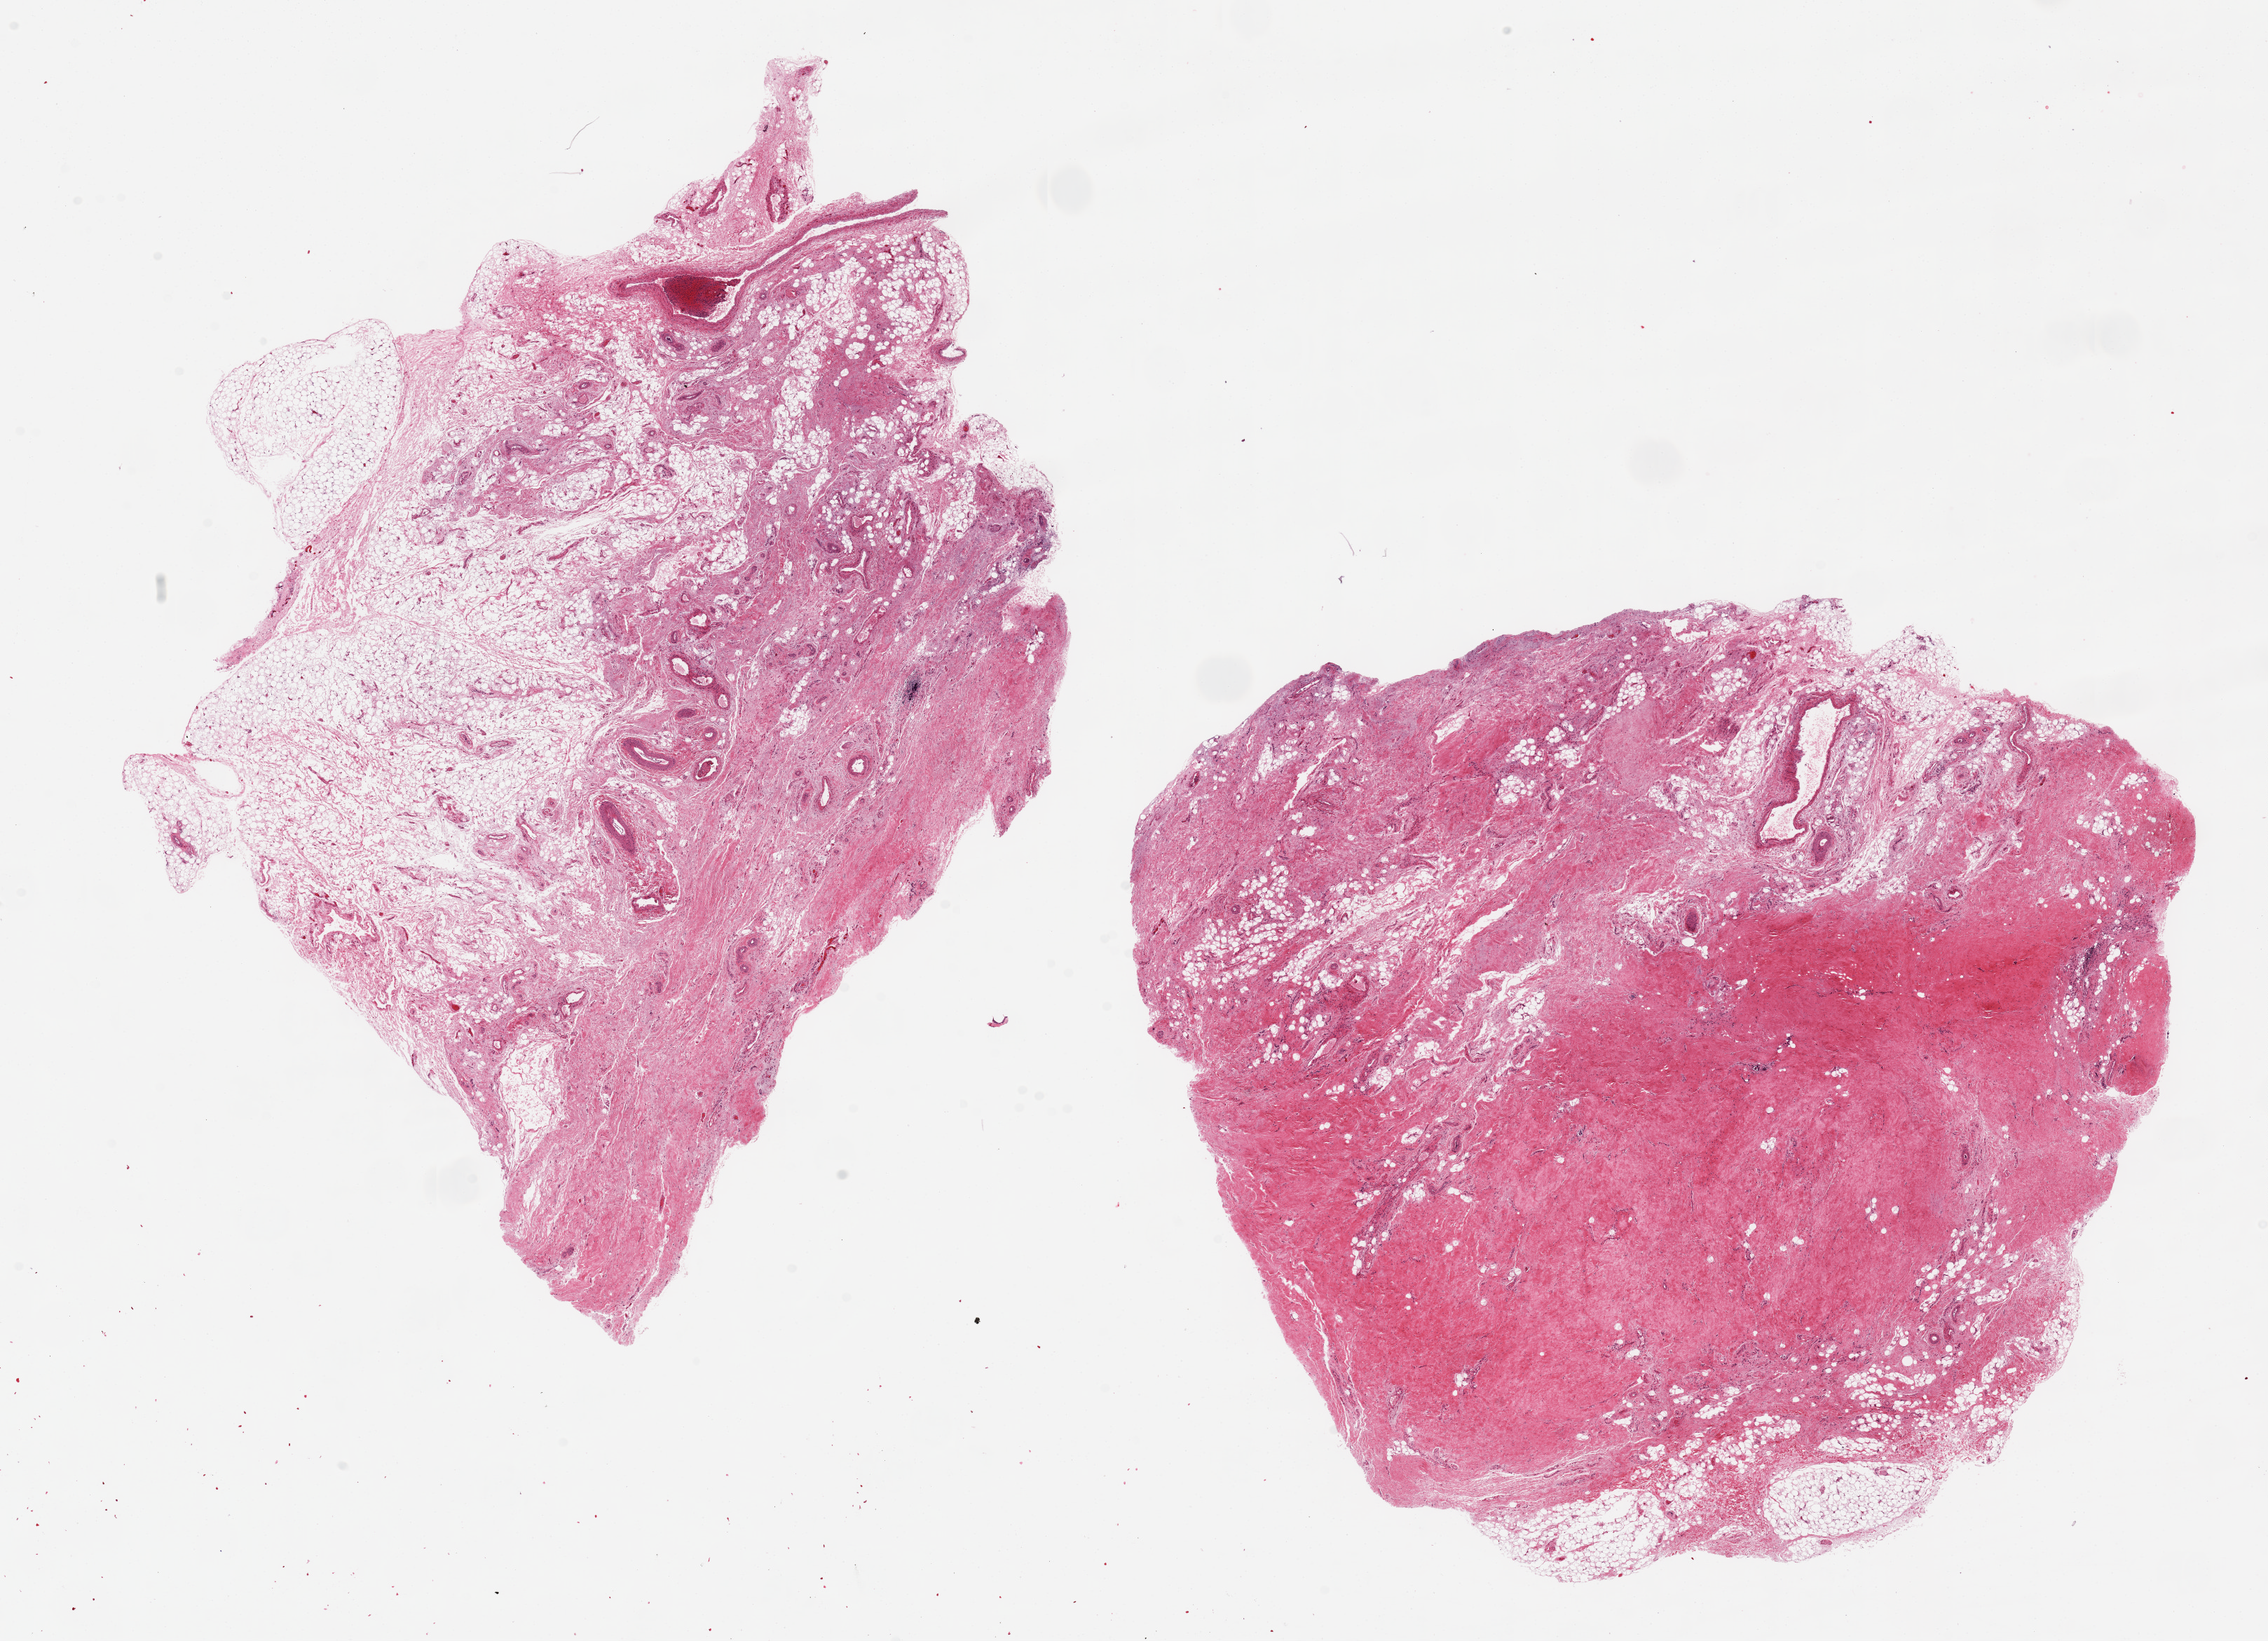
Haematoxylin and eosin whole-slide image, a low-resolution overview of the entire scanned area, about 25.6 x 18.5 mm (from a 20x scan); PAXgene-fixed paraffin-embedded (PFPE) section; section of thyroid (target tissue); donor tissue sample. Female donor.
Pathologist's review note for this sample: 2 pieces of fibroadipose tissue, unknown provenance.